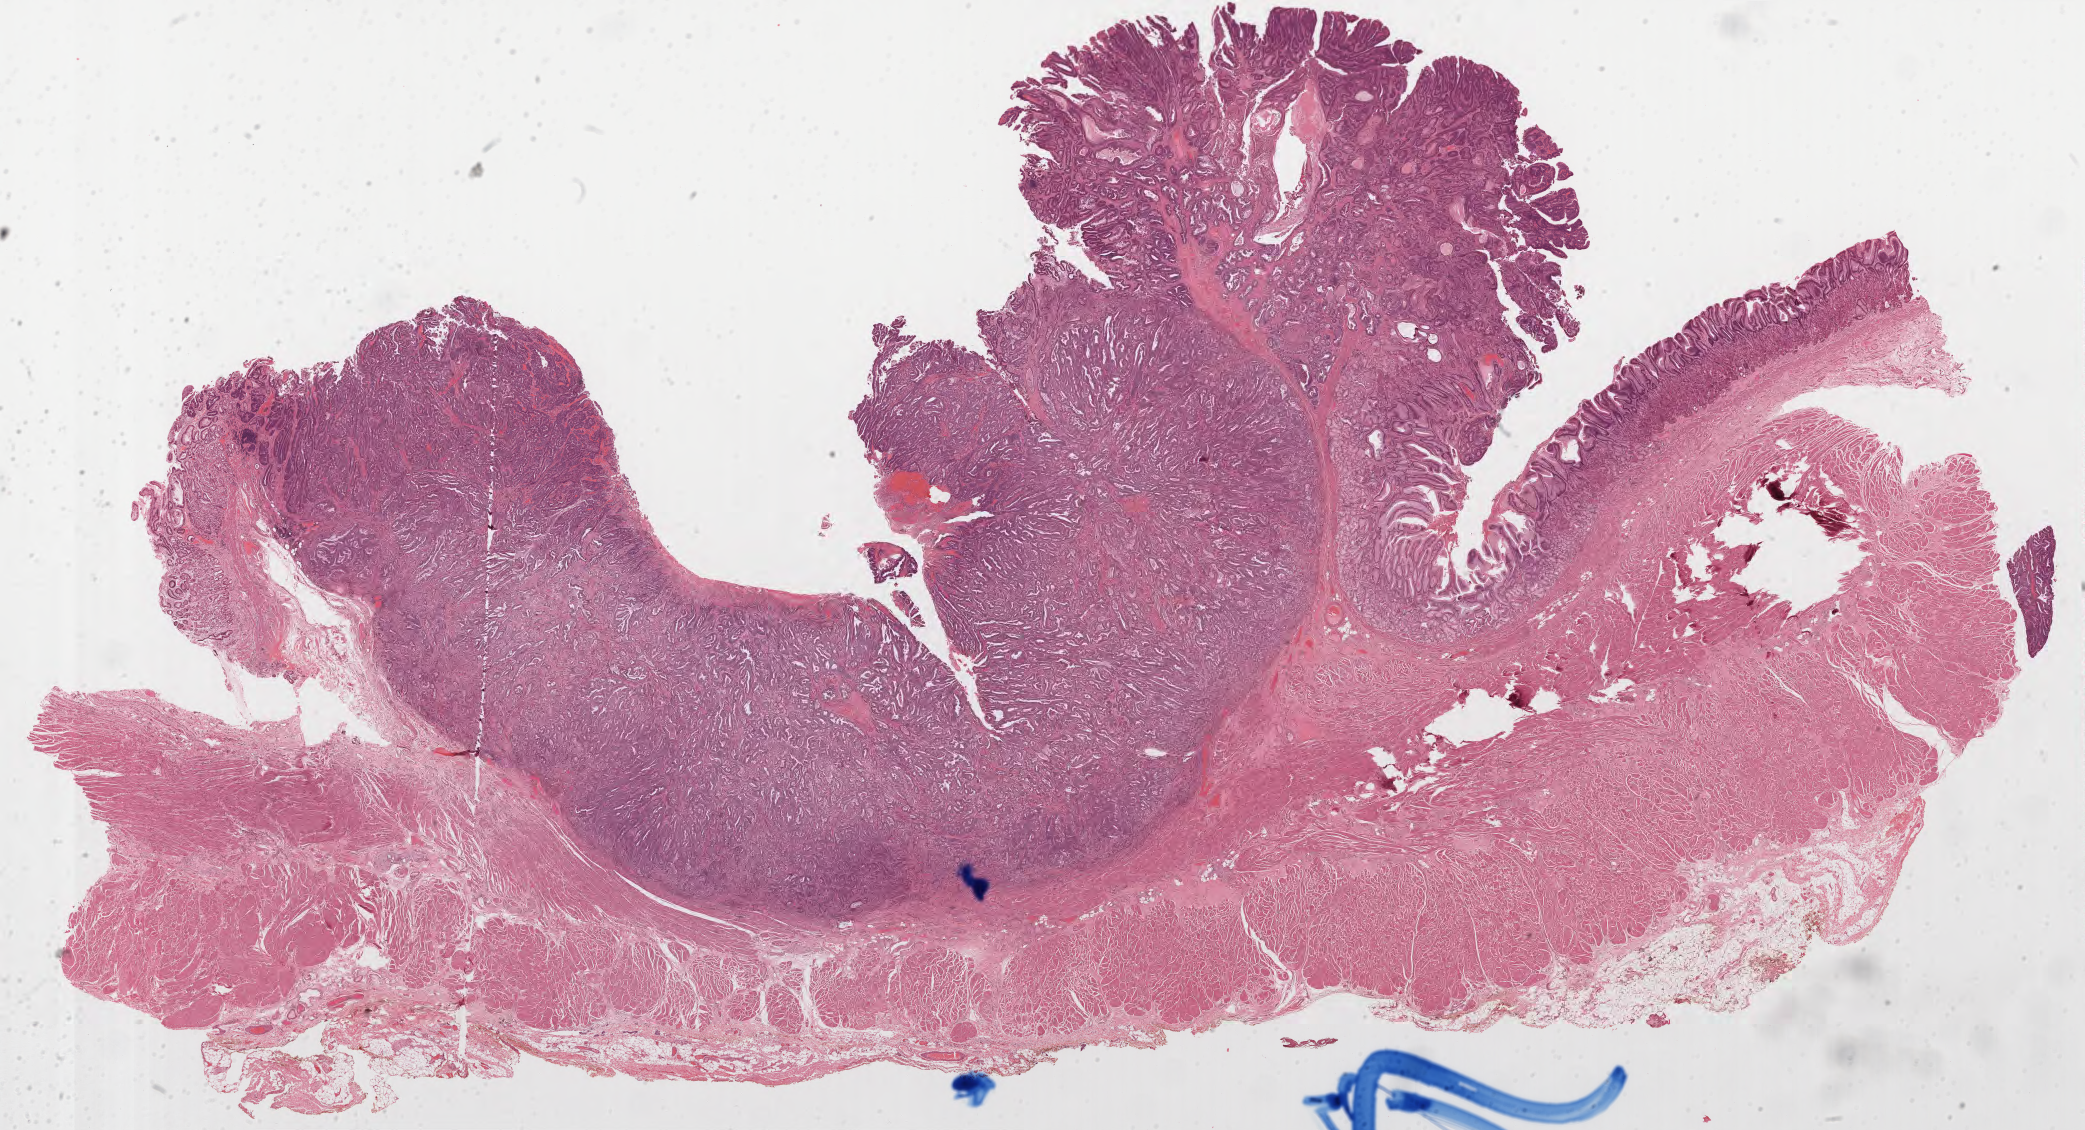
Hematoxylin and eosin (H&E) stained whole-slide image, shown as a low-resolution overview of the whole scanned area (about 33.6 x 18.2 mm, from a 40x scan). Formalin-fixed paraffin-embedded (FFPE) diagnostic section. Primary tumour sample from the esophagus. Male, age 53 years at initial diagnosis. Histologic grade: G2 (moderately differentiated).
AJCC pathologic stage: IIB (7th edition). Lymph nodes positive (case pathology): 2 of 18 examined. Histologic diagnosis: Adenocarcinoma, NOS (lower third of esophagus).